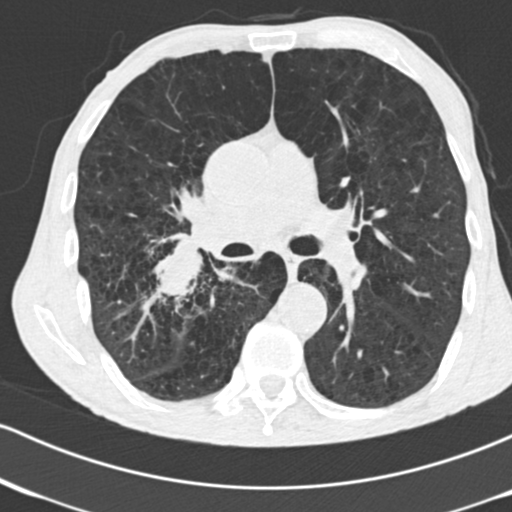
Chest CT (low-dose screening protocol), one axial image. Second annual screen. Lung window (W 1500 / L -600 HU). 2 mm slice thickness. 120 kVp. Slice 85 of 182 in the series. Male, age 64 years at enrolment. Current smoker at enrolment.
Expert reader's lesion annotation, bounding box (x1, y1, x2, y2) in pixels: (133, 232, 237, 327). Screening reader's record for this exam (one nodule recorded; not confirmed to be the boxed lesion): non-calcified nodule or mass ≥4 mm, 52 × 37 mm, spiculated (stellate) margins, soft tissue attenuation, pre-existing on the prior screen: no. Official screen result: positive, other. Lung cancer was diagnosed 28 days after this screen: adenocarcinoma, NOS, right lower lobe, stage IV (AJCC 6th edition), 60 mm at pathology.